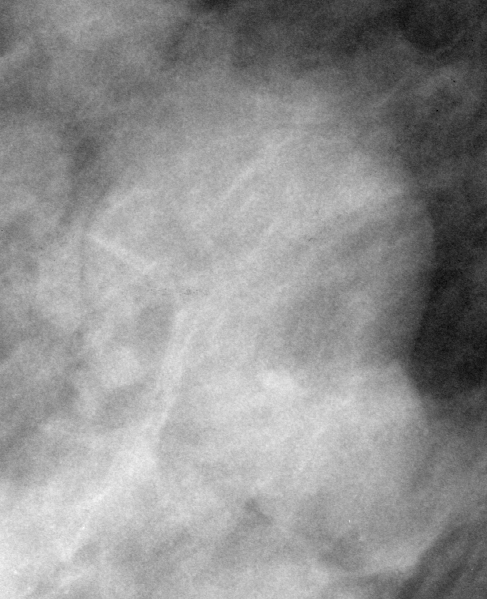
Region of interest cut from a scanned film mammogram (one marked finding), right breast, MLO view, BI-RADS breast density category 3 (scale 1–4).
Mass, shape lobulated, margins circumscribed; BI-RADS assessment category 3; subtlety rating 4 on a 1 (subtle) to 5 (obvious) scale; pathology result (as recorded, not read from the image): benign.